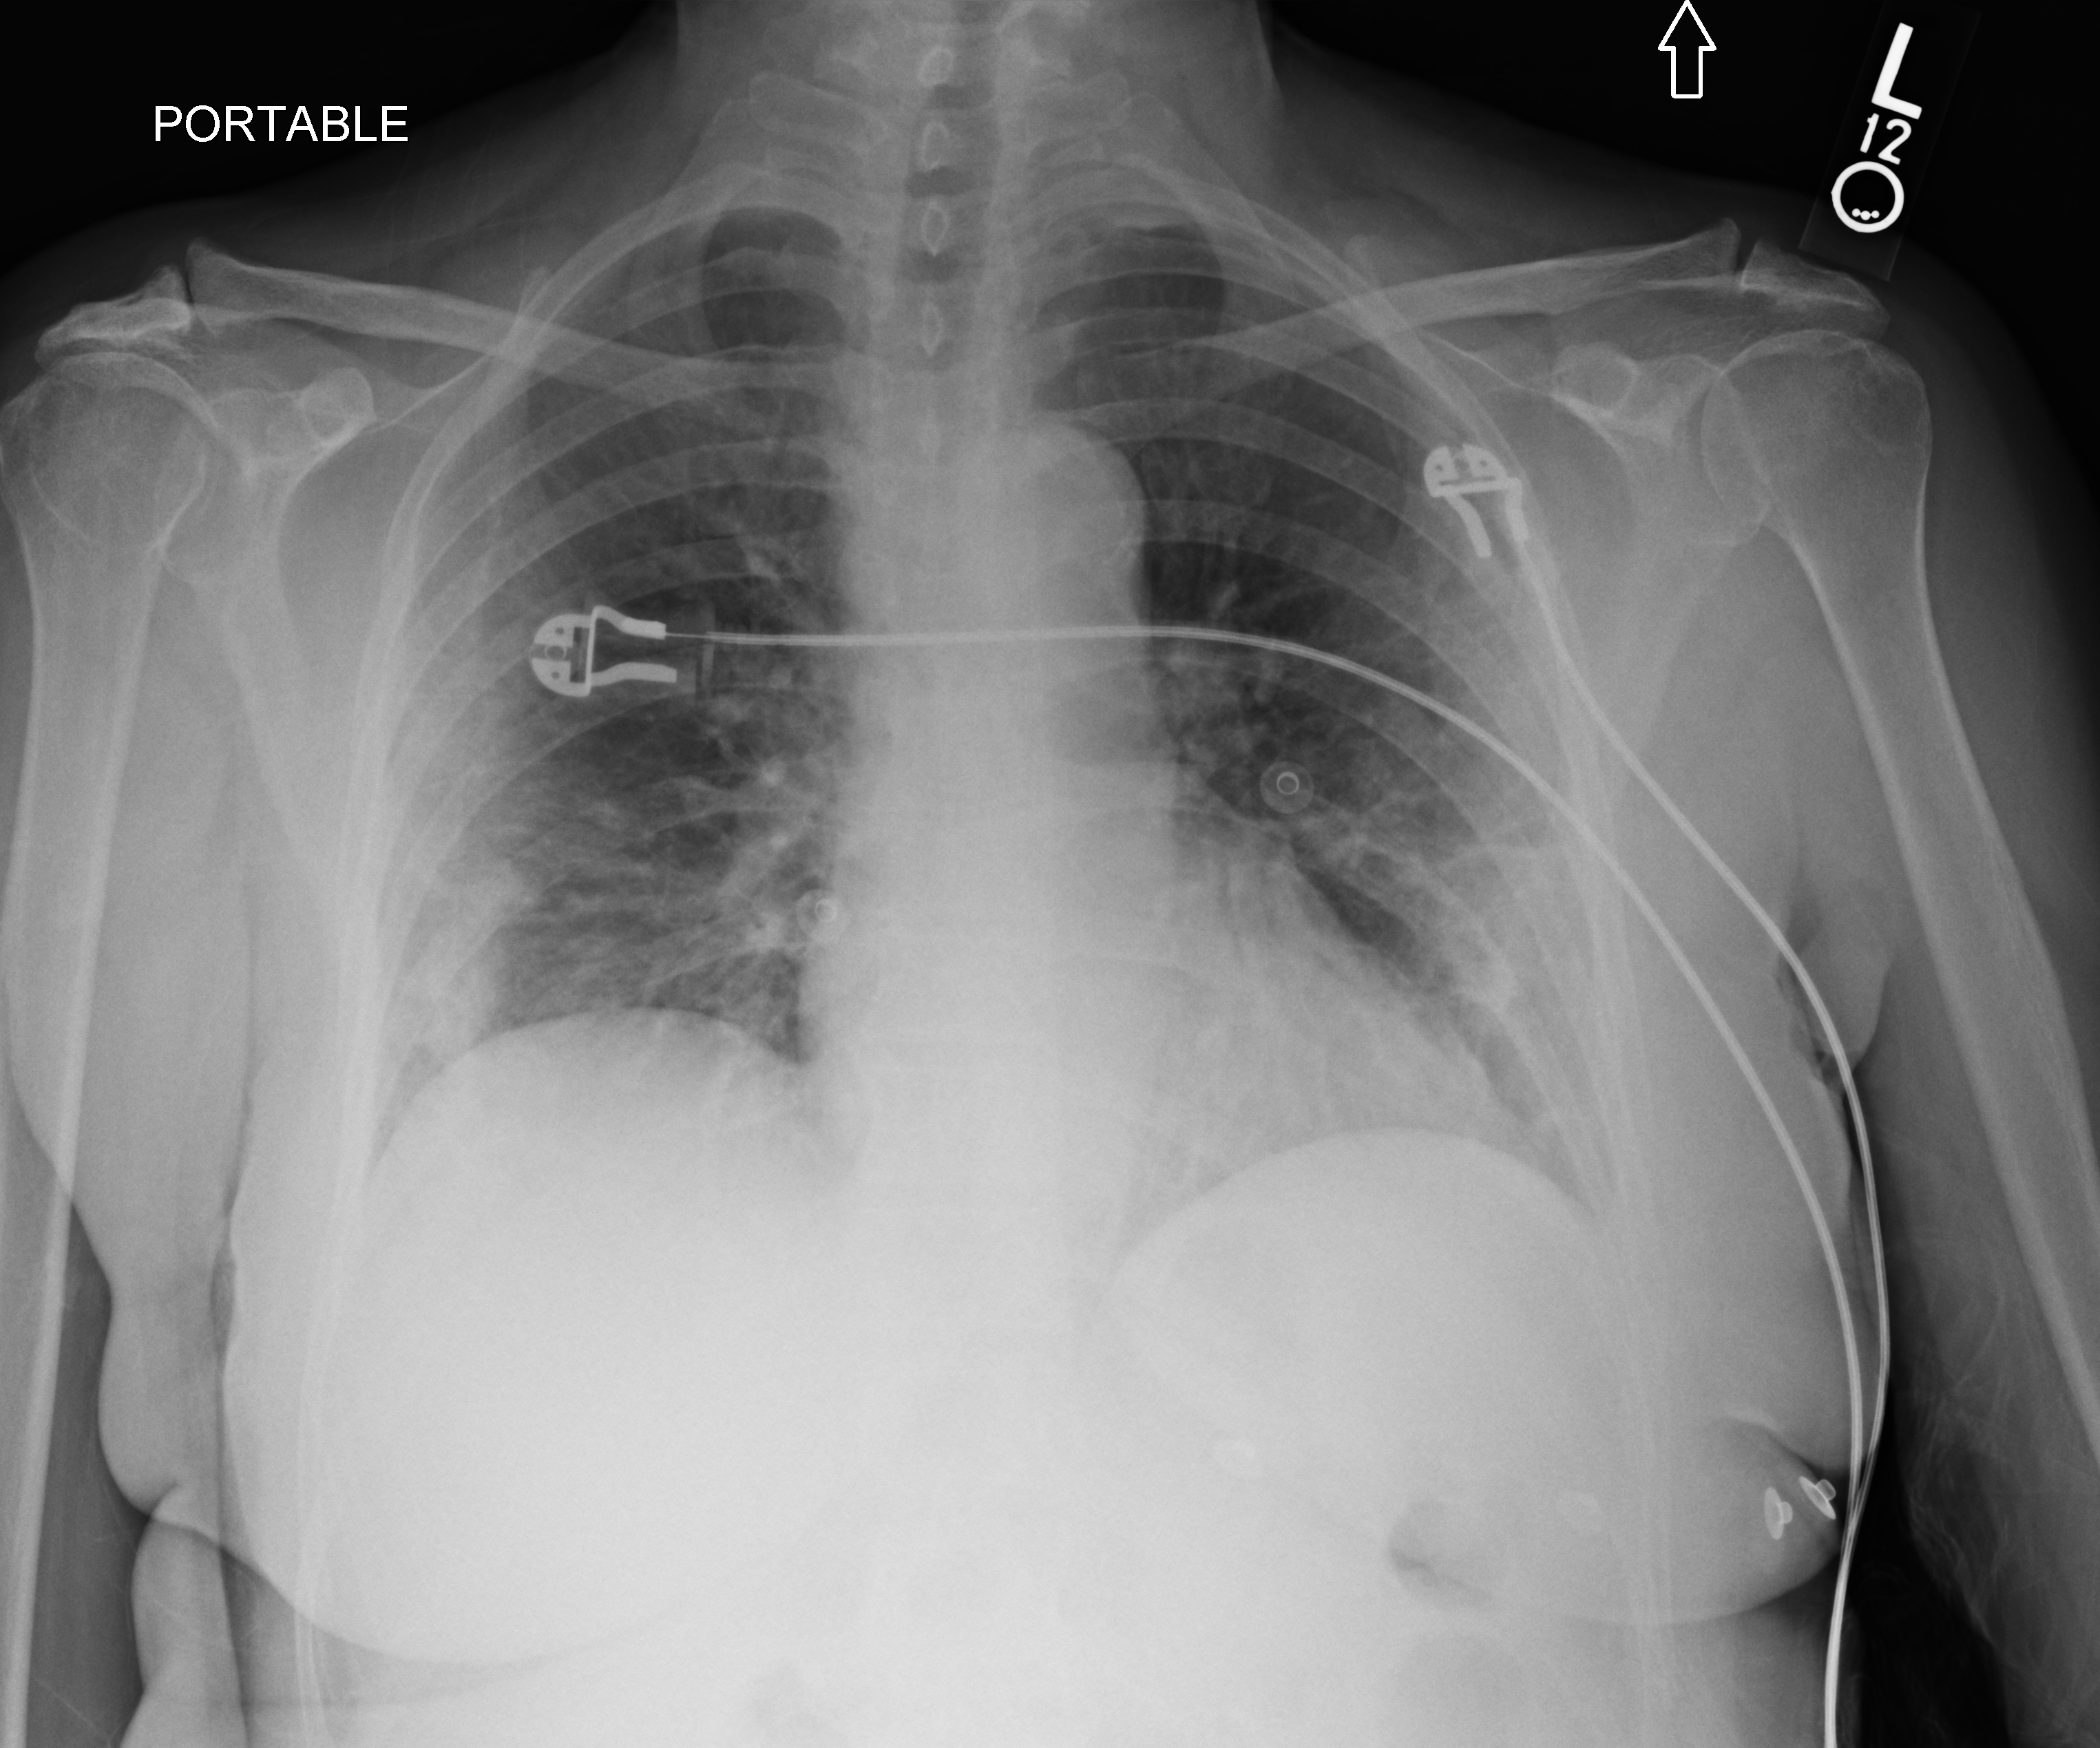
Chest X-ray (portable), anteroposterior (AP) projection. Patient hospitalised with COVID-19; female, aged 60–74 years.
Admission-level facts for this patient (not findings on this image; timing relative to this image not recorded): smoking status (admission record): former; COPD (admission record): no; mechanically ventilated during this hospital stay: yes.